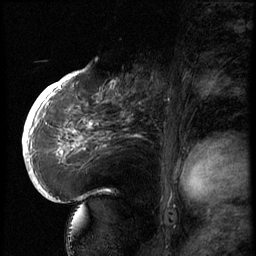
Breast MRI (dynamic contrast-enhanced), one sagittal slice; position 35 of 66 along the scan axis; 3 images stored at this slice position (order not interpretable as contrast timing); 1.5 T; TE 4.2 ms, TR 8.9 ms; 256 × 256 image matrix. Patient: female, 56 years. From the clinical record (not read from this slice): setting: breast cancer imaged before/during neoadjuvant chemotherapy.
Annotated regions visible in this slice (semi-automatic segmentation, software-assisted and operator-edited):
- analysis volume of interest (the breast-tissue region the enhancement analysis was run in; not a lesion): bounding box <129,62,194,127> (left, top, right, bottom; pixels)
- tumour enhancement mask (voxels above the 140 % enhancement threshold inside the analysis volume of interest): <129,73,160,123>